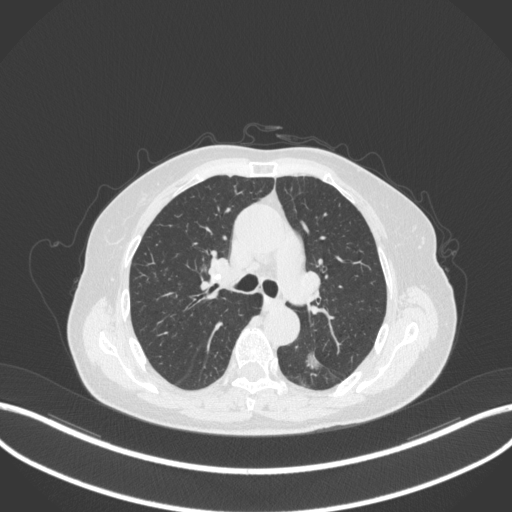
Chest CT, one axial slice. Position 196 of 352 along the scan axis. Reconstruction kernel B31f. Lung window (W 1500 / L -600 HU). 1 mm slice thickness. 512 × 512 image matrix, field of view 400 × 400 mm. Female patient, age 70 years. From the clinical record (not read from this slice): clinical TNM (as recorded): T1c N0 M0.
Outlined on this slice (bounding box drawn by a radiologist):
- lung tumour (recorded histology: adenocarcinoma): bounding box <302,345,328,371> (left, top, right, bottom; pixels)